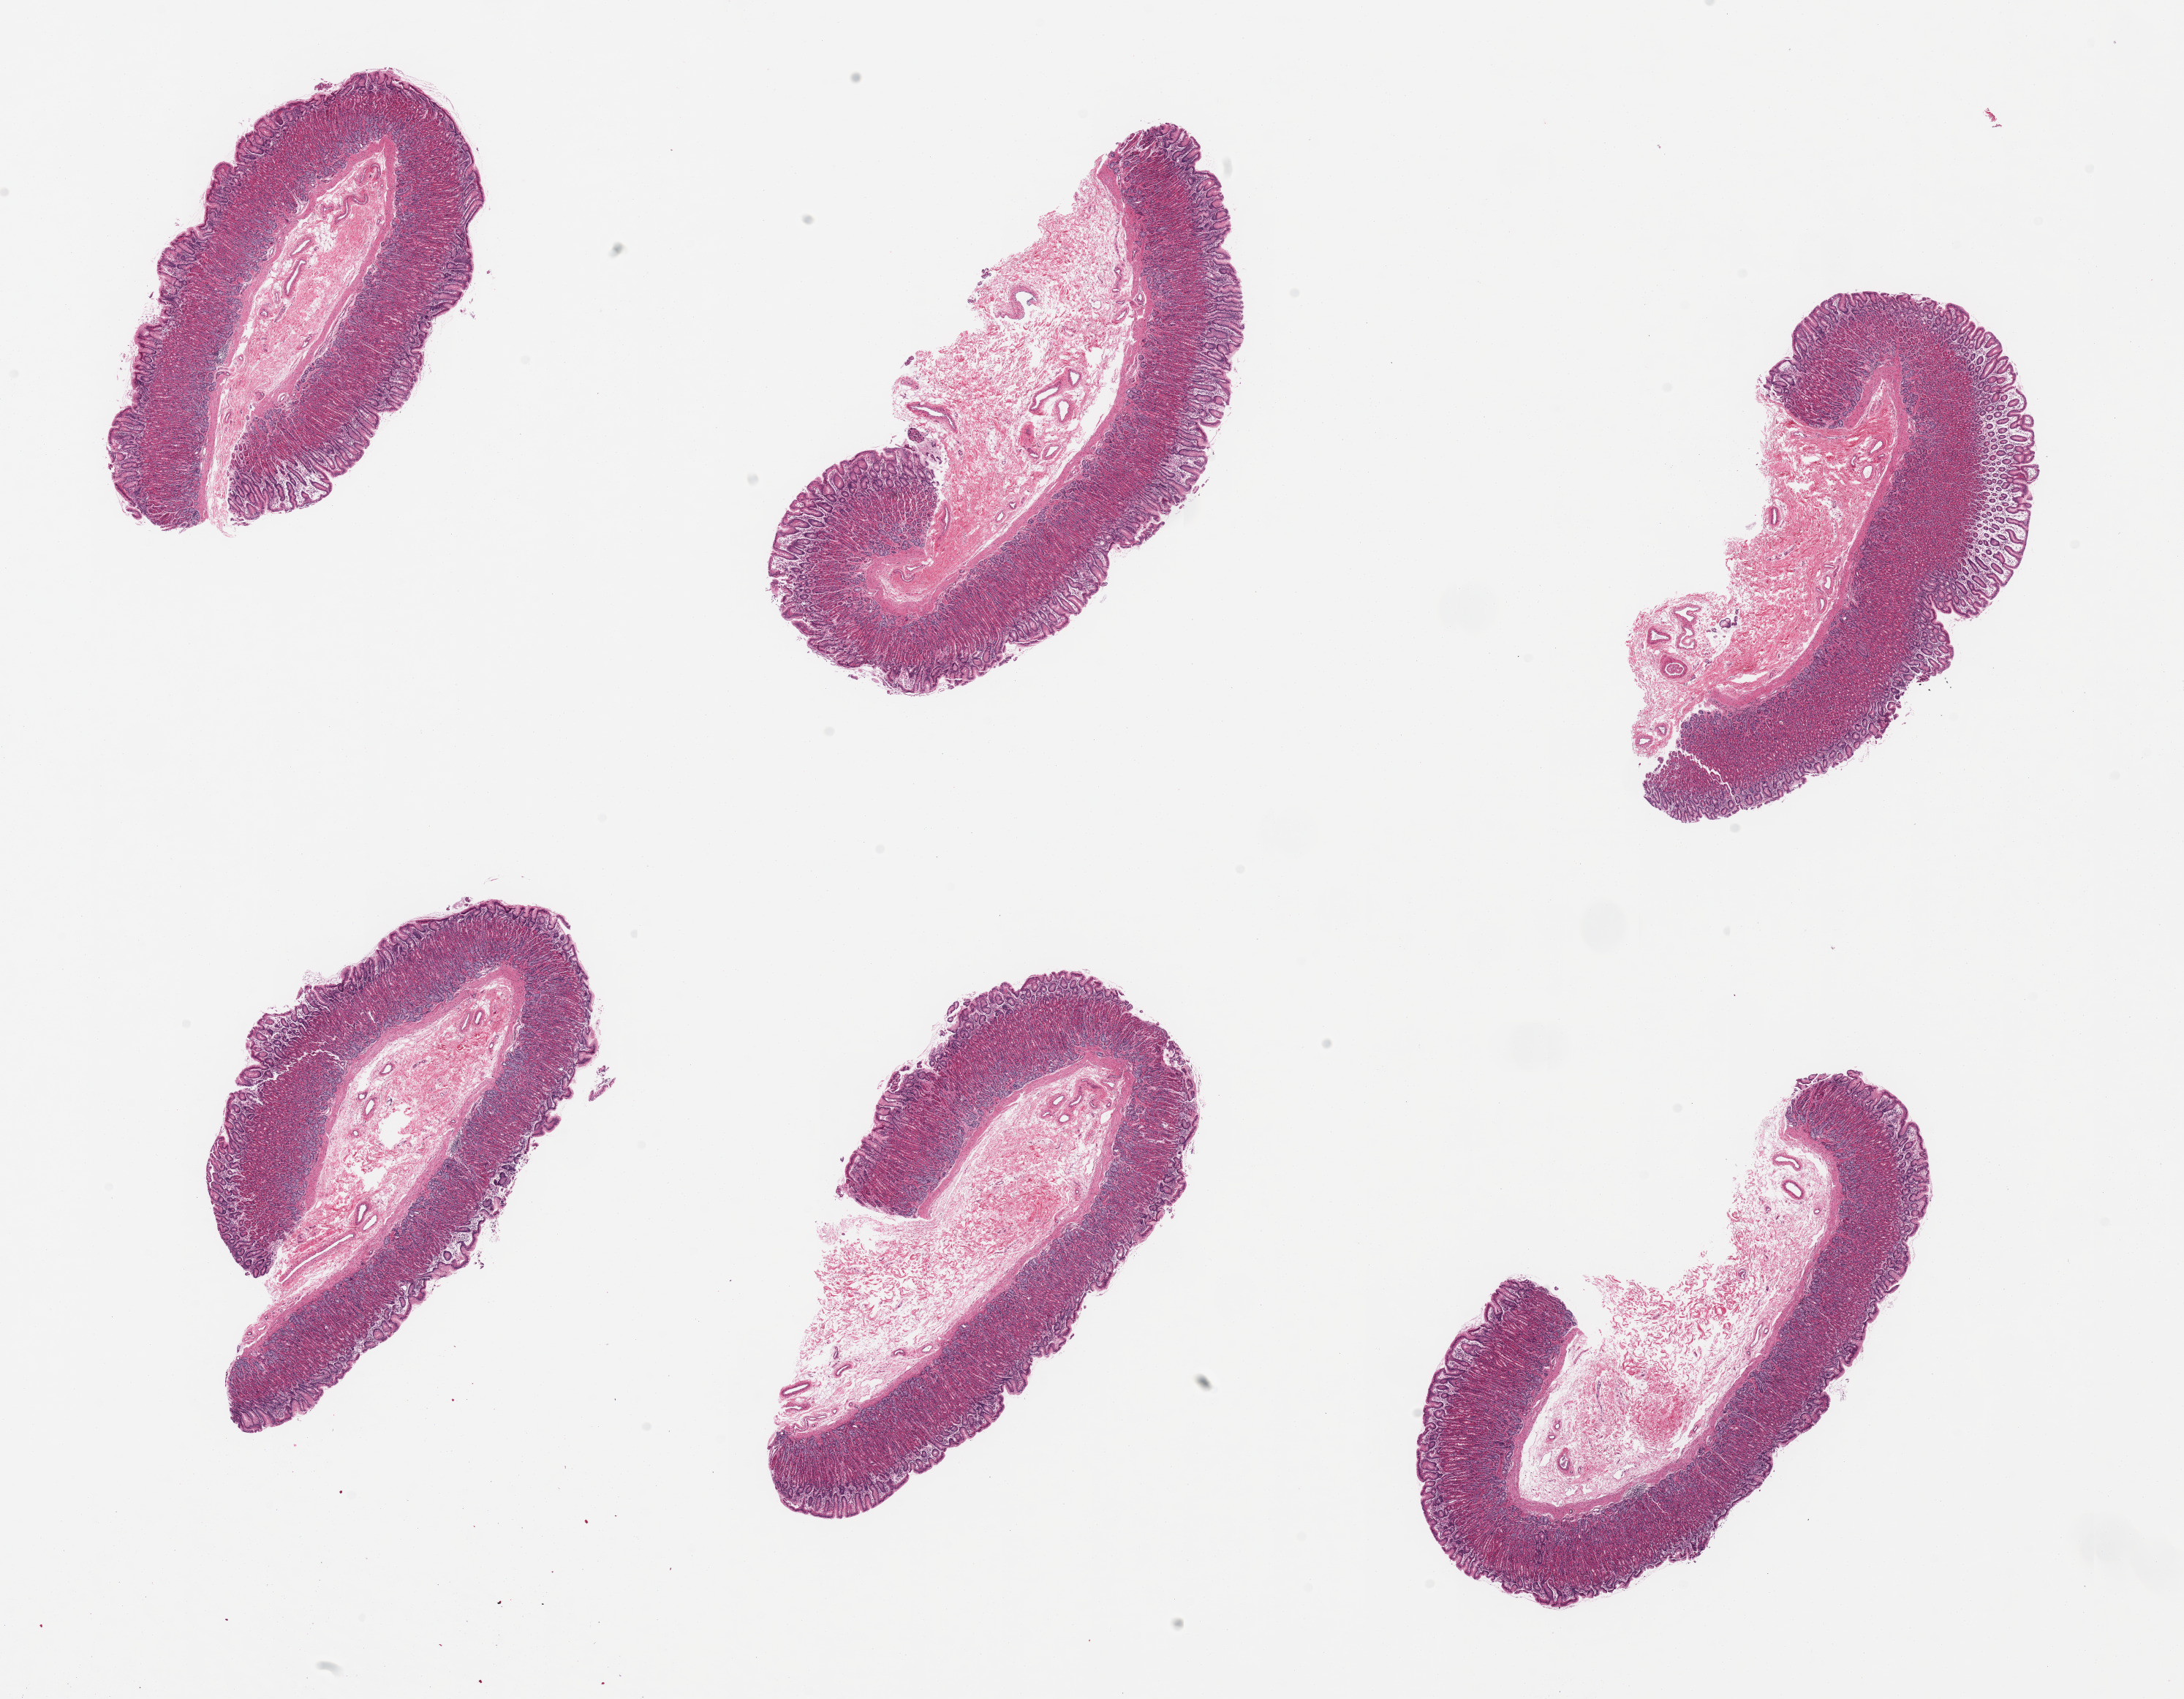
Digitized H&E-stained section, brightfield, low-resolution overview of the scanned area, about 23.6 x 18.4 mm (slide scanned at 20x). PAXgene-fixed paraffin-embedded (PFPE) section. Sampled site (target tissue): stomach. Donor tissue sample. Donor: female.
* review note (as recorded): 6 pieces, target mucosa well-fixed, good specimen, up to ~1mm, 50-60% thickness